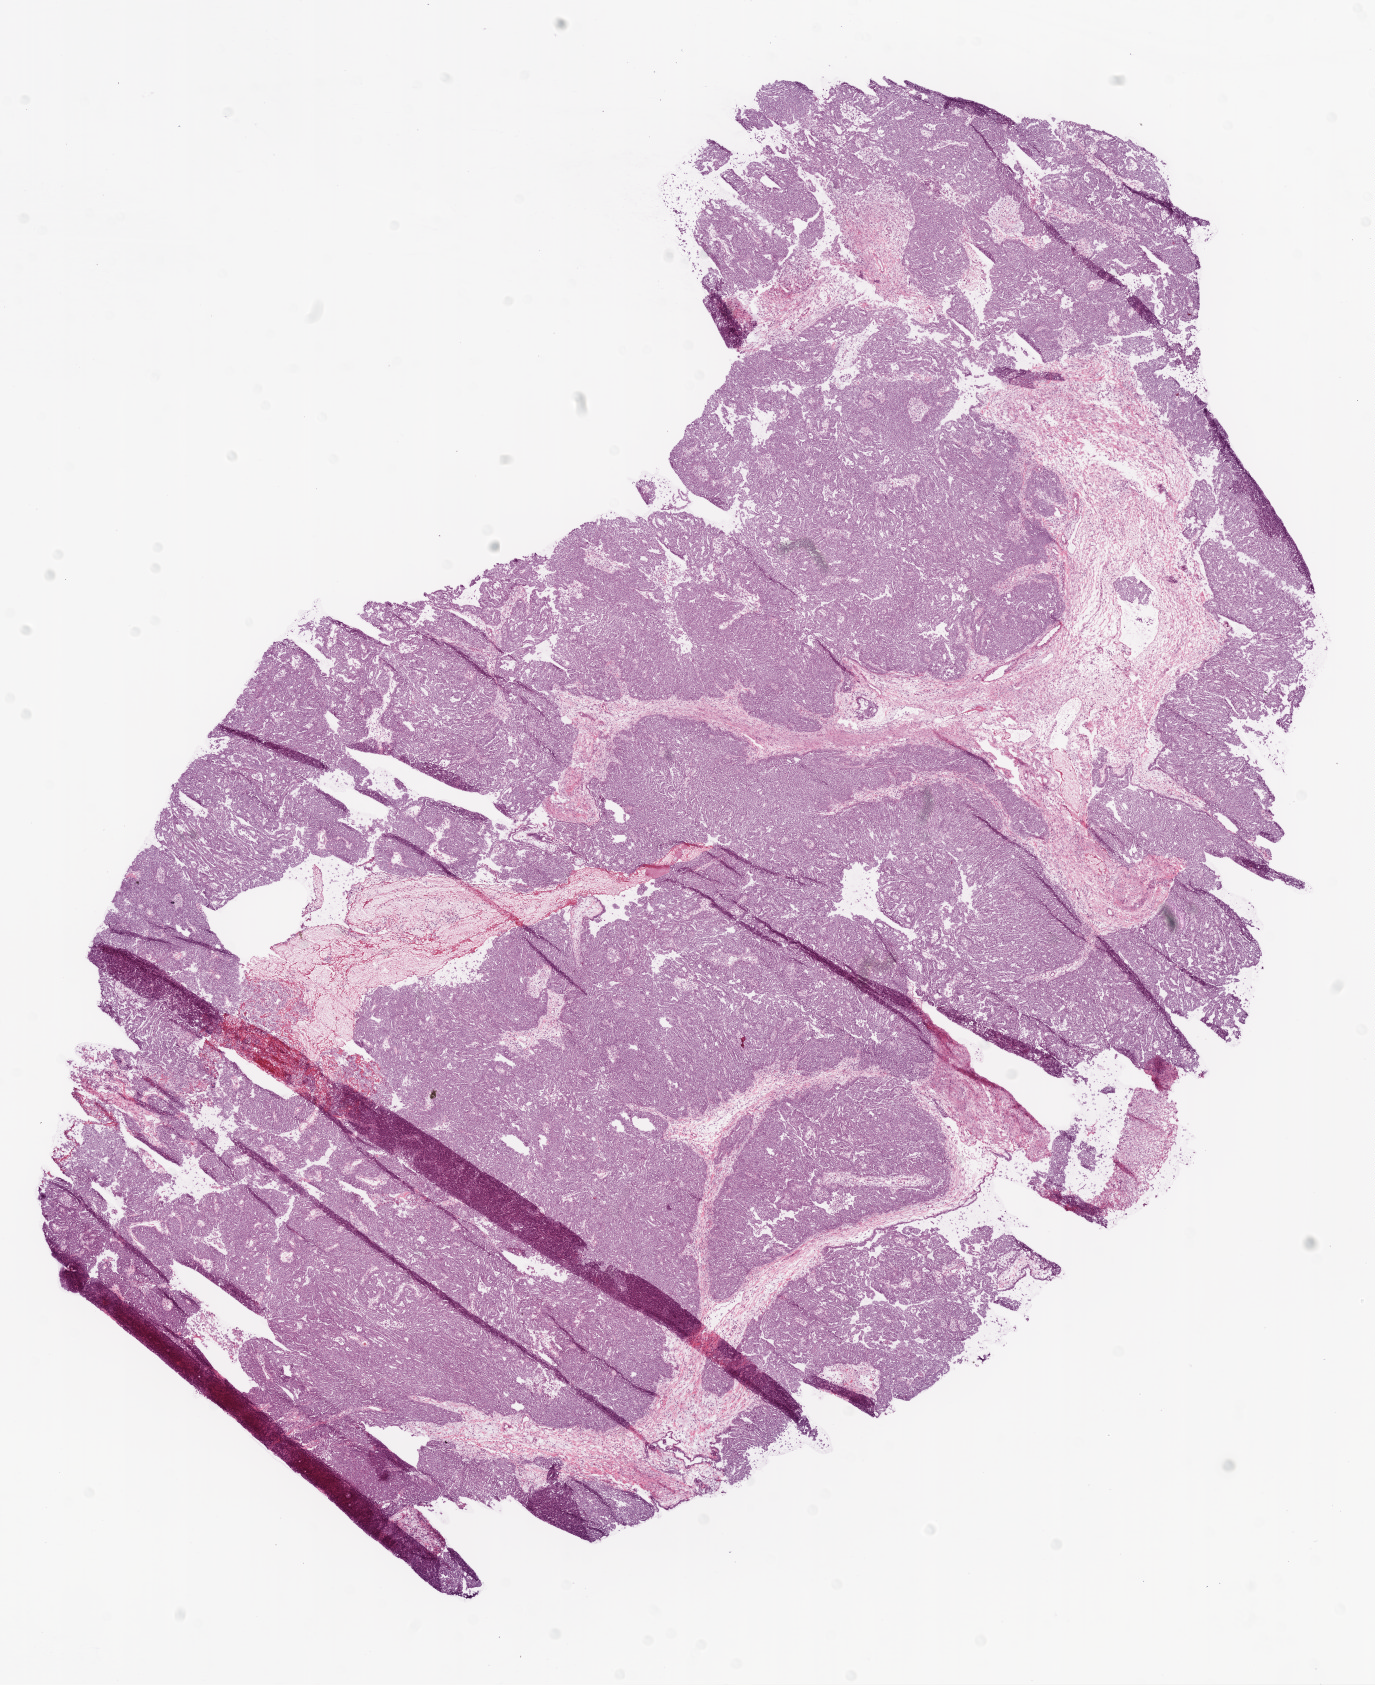
Digitized H&E tissue section (whole slide) — whole scanned area (about 11.0 x 13.5 mm, acquisition: 20x scan) shown as a low-resolution overview, frozen section, sample: primary tumour, ovary. Patient: female, age at initial diagnosis 58 years. Histologic grade: G3 (poorly differentiated). Pathologist review of this section (percent, as recorded): tumour cells 87%, tumour nuclei 95%, normal cells 10%, stromal cells 0%, necrosis 3%.
- FIGO stage: IV
- diagnosis: Serous cystadenocarcinoma, NOS